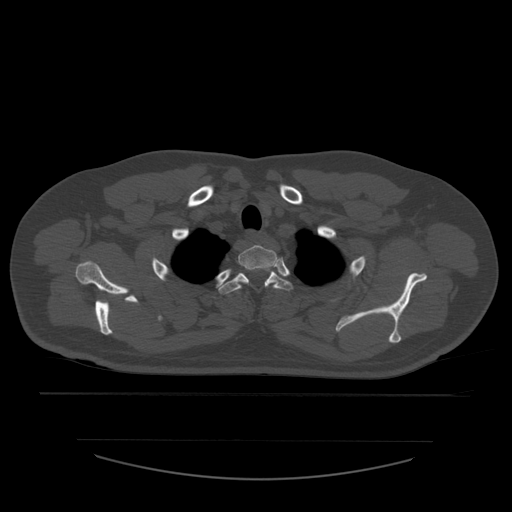
CT including the spine, one axial slice; position 457 of 532 along the scan axis; 120 kVp; bone window (W 1800 / L 400 HU); 1.25 mm slice thickness; 512 × 512 image matrix. Patient age 44 years. From the clinical record (not read from this slice): primary cancer: soft tissue sarcoma.
Annotated regions visible in this slice (semi-automatic segmentation, software-assisted and operator-edited):
- T1 vertebra: bounding box [x1, y1, x2, y2] px = [238, 245, 278, 271]
- T2 vertebra: [219, 270, 293, 294]